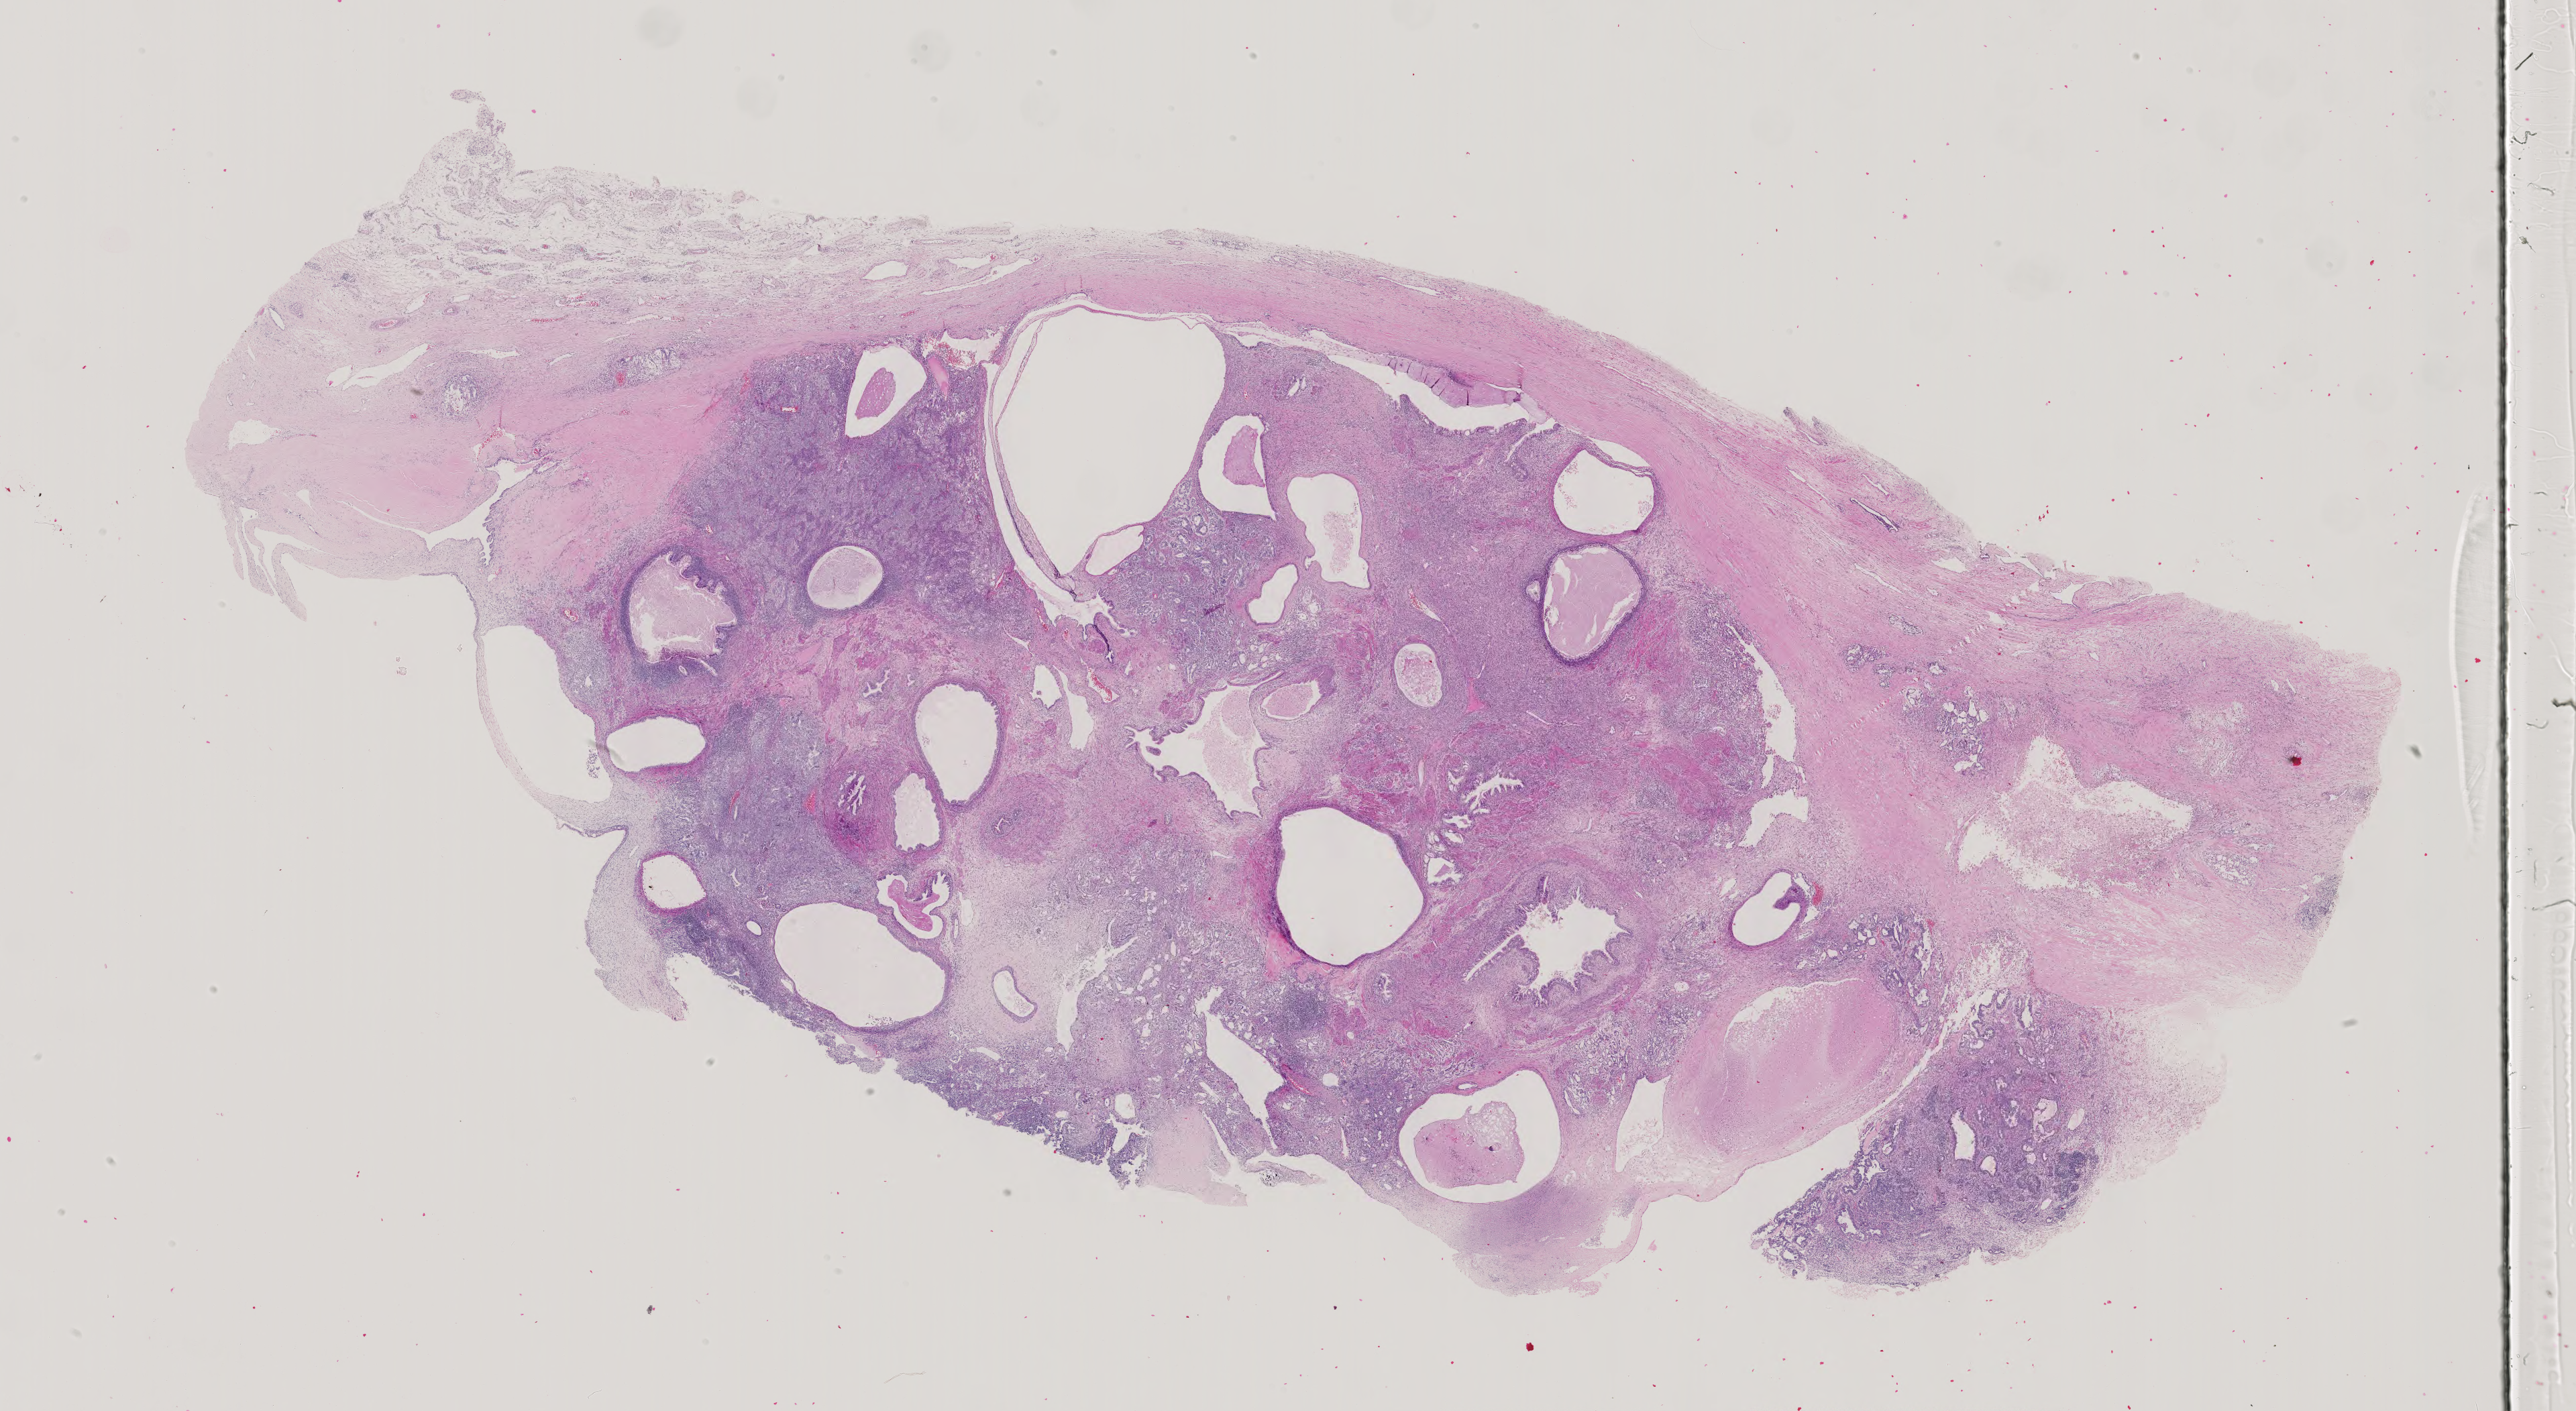
H&E whole-slide image — low-resolution overview of the scanned area, about 28.0 x 15.3 mm (acquisition: 40x scan). Patient sex: male.
• specimen: formalin-fixed paraffin-embedded (FFPE) diagnostic section; primary tumour sample from the testis